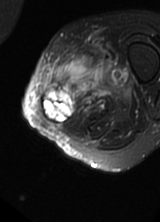
MRI of an extremity soft-tissue mass, one axial slice. Slice 16 of 69 in the series (ordered by position). T2-weighted fat-saturated. MR volume resampled by the dataset authors to the PET/CT grid (not the native acquisition matrix). 3.27 mm slice thickness. 160 × 222 image matrix, field of view 156 × 217 mm. Female patient. From the clinical record (not read from this slice): histological type: pleomorphic leiomyosarcoma; grade: high; site of the primary tumour: left thigh.
Annotated regions visible in this slice (expert contour drawn on MRI and transferred to this co-registered scan by the dataset authors):
- gross tumour volume including surrounding oedema: bounding box <41,54,126,124> (left, top, right, bottom; pixels)
- gross tumour volume (mass): <41,86,74,124>